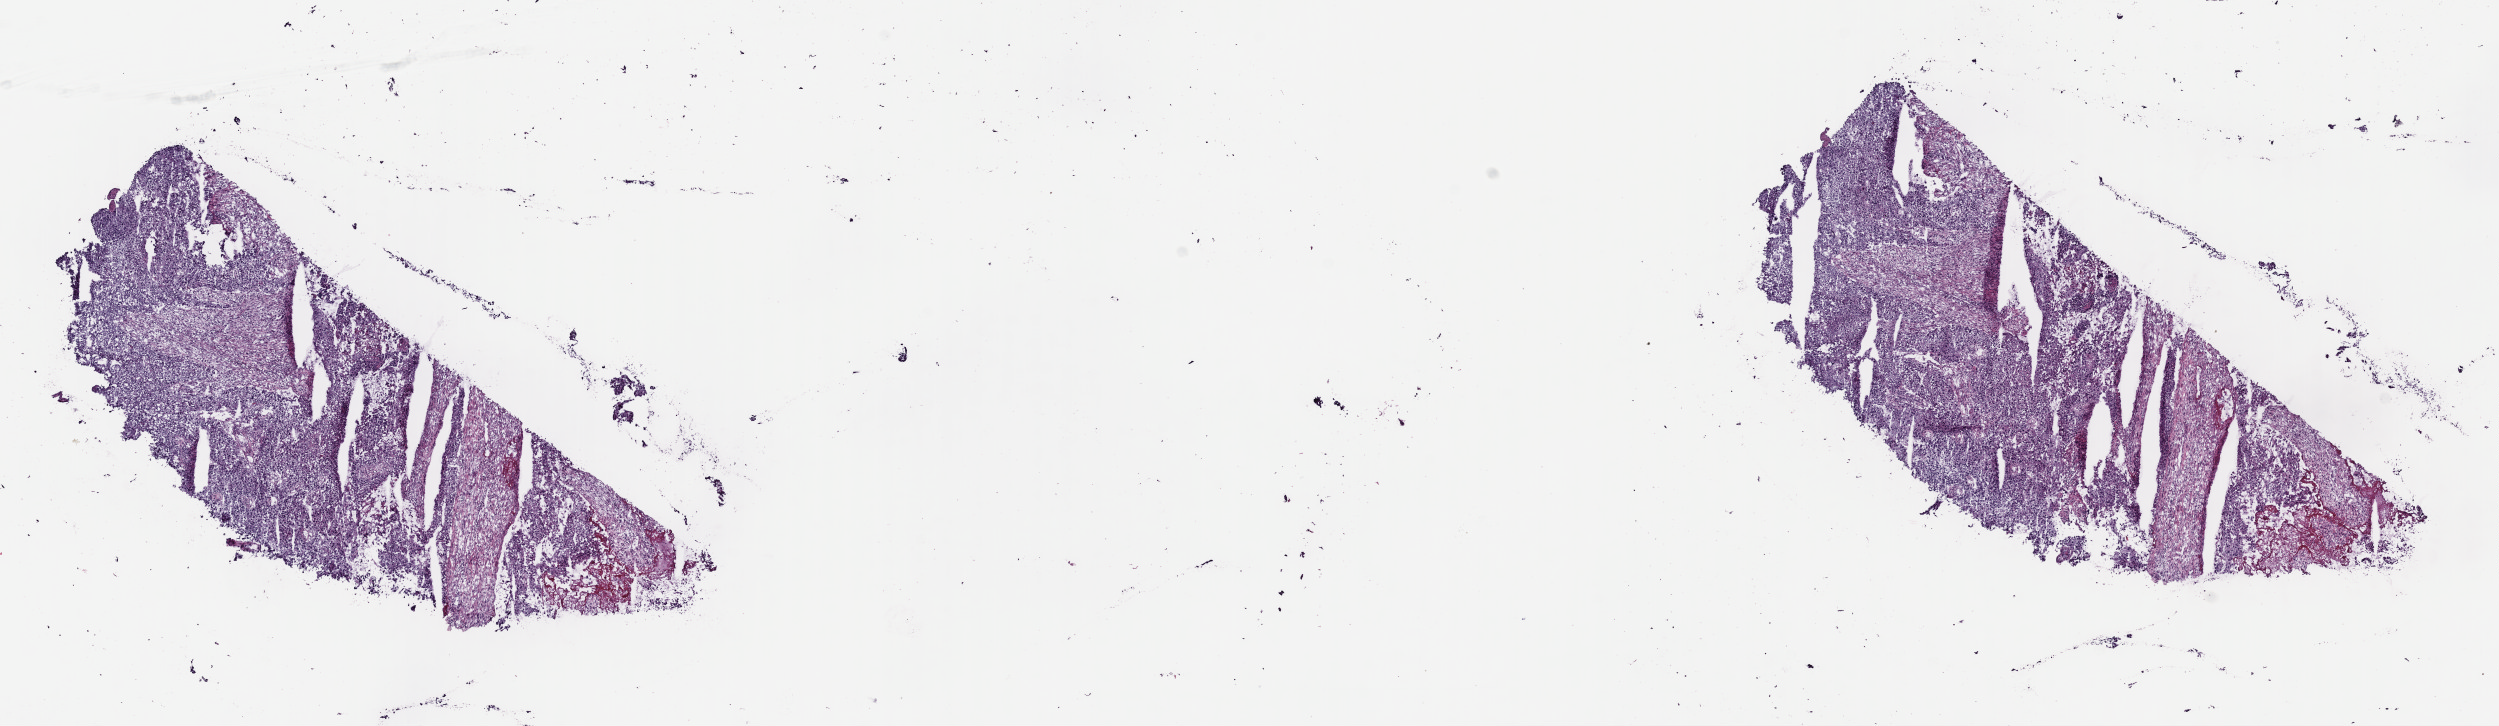
H&E-stained whole-slide image — low-resolution overview of the scanned area, about 19.7 x 5.7 mm, frozen section from the top of the tissue portion, sample: primary tumour, bladder. Male, age 72 years at initial diagnosis. Histologic grade: high grade. Pathologist review of this section (percent, as recorded): tumour cells 80%, tumour nuclei 80%, normal cells 0%, stromal cells 20%, necrosis 0%. Infiltration values recorded for this section: lymphocyte infiltration 5%, monocyte infiltration 0%, neutrophil infiltration 0%.
TNM: T3a N0 MX. Histologic diagnosis: Transitional cell carcinoma (trigone of bladder). AJCC pathologic stage: III.